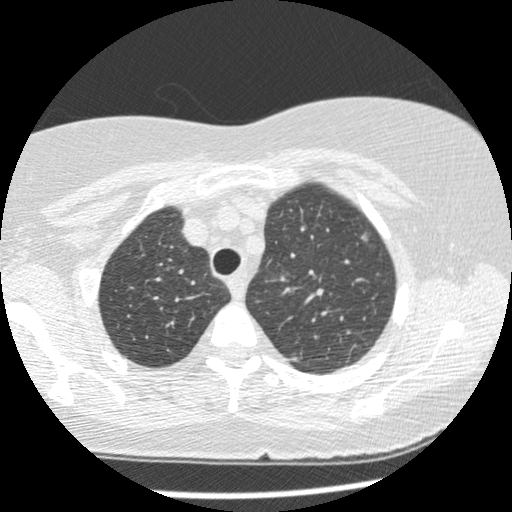
Low-dose screening chest CT, one axial slice; slice 188 of 241 in the series (ordered by position); reconstruction kernel STANDARD; 120 kVp; lung window (W 1500 / L -600 HU); 512 × 512 image matrix.
Annotated regions visible in this slice (expert manual segmentation):
- lesion 2 (tumor, upper lobe of left lung): bounding box (x1, y1, x2, y2) in pixels: (361, 233, 368, 241)